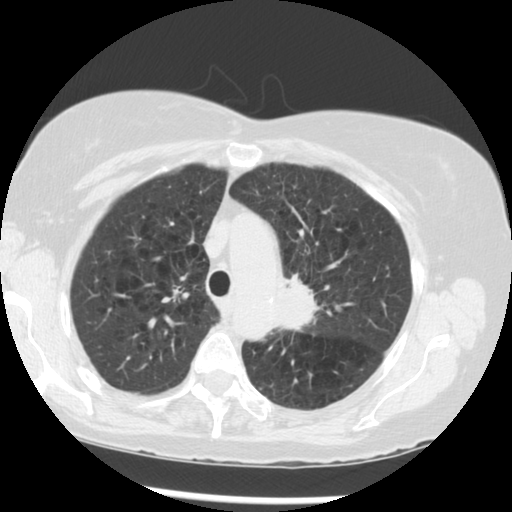
Chest CT (low-dose screening protocol), one axial image; third annual screen; lung window (W 1500 / L -600 HU); 120 kVp; slice 212 of 283 in the series. Female, age 70 years at enrolment. Current smoker at enrolment.
• Expert-annotated lung lesion, bounding box <268,265,361,355> (left, top, right, bottom; pixels).
• The exam's reader record, not a measurement of the box and not confirmed to be the same lesion: non-calcified nodule or mass ≥4 mm, left upper lobe, 32 × 26 mm, spiculated (stellate) margins, soft tissue attenuation, pre-existing on the prior screen: yes; interval growth: yes.
• Official screen result: positive, other.
• Later outcome: lung cancer diagnosed 24 days after this screen — neoplasm, malignant, left upper lobe, stage IIIB (AJCC 6th edition), 40 mm at pathology.